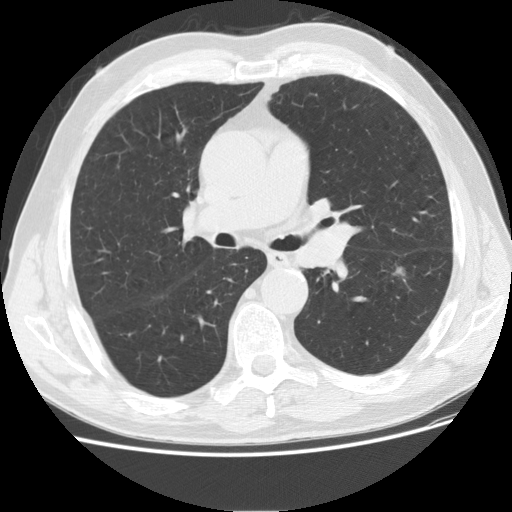
Low-dose screening chest CT, axial slice, second screening round (one year after baseline), lung window (W 1500 / L -600 HU), 2.5 mm slice thickness, standard (soft-tissue) reconstruction kernel (STANDARD), 120 kVp, 512 × 512 image matrix, field of view 360 × 360 mm. Male participant, aged 73 years at enrolment. Current smoker at enrolment.
- Expert reader's lesion annotation, bounding box [x1, y1, x2, y2] px = [362, 251, 428, 306].
- Reader record for this screening exam (exam-level; its link to the box is not recorded): non-calcified nodule or mass ≥4 mm, left lower lobe, 16 × 10 mm, smooth margins, soft tissue attenuation, pre-existing on the prior screen: yes; interval growth: yes.